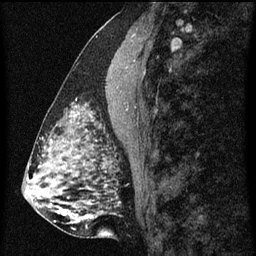
Breast MRI (dynamic contrast-enhanced), one sagittal slice; slice 25 of 60 in the series (ordered by position); dynamic contrast-enhanced series, image 2 of 3 at this slice position (ordered by acquisition); 1.5 T; TE 4.2 ms, TR 8 ms; 256 × 256 image matrix. Patient: female, 51 years.
Structures marked on this image (semi-automatically segmented with operator editing):
- analysis volume of interest (the breast-tissue region the enhancement analysis was run in; not a lesion): bounding box (x1, y1, x2, y2) in pixels: (61, 106, 101, 129)
- tumour enhancement mask (voxels above the 70 % enhancement threshold inside the analysis volume of interest): (69, 106, 93, 121)